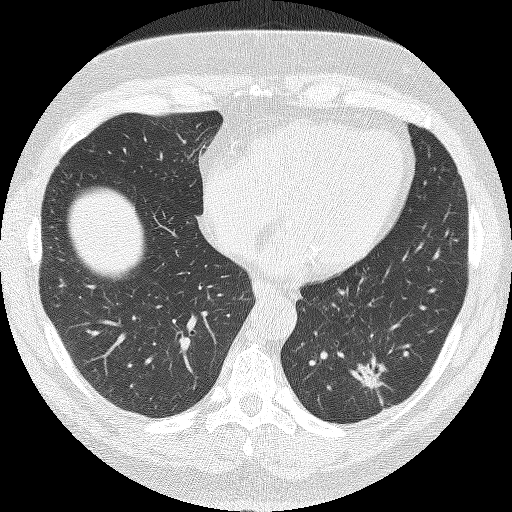
Axial slice from a low-dose chest CT screening exam, first (baseline) screen, lung window (W 1500 / L -600 HU), 2 mm slice thickness, lung (sharp) reconstruction kernel (FC51), slice 96 of 140 in the series. Male, age 62 years at enrolment.
- Expert-annotated lung lesion, box from (x=348, y=354) to (x=405, y=406) px.
- The screening reader recorded 2 non-calcified nodules or masses ≥4 mm on this exam (left lower lobe, right upper lobe); which of them this box marks is not recorded.
- Lung cancer was diagnosed 90 days after this screen: adenocarcinoma, NOS, left lower lobe, moderately differentiated (G2), stage IA (AJCC 6th edition), 30 mm at pathology.